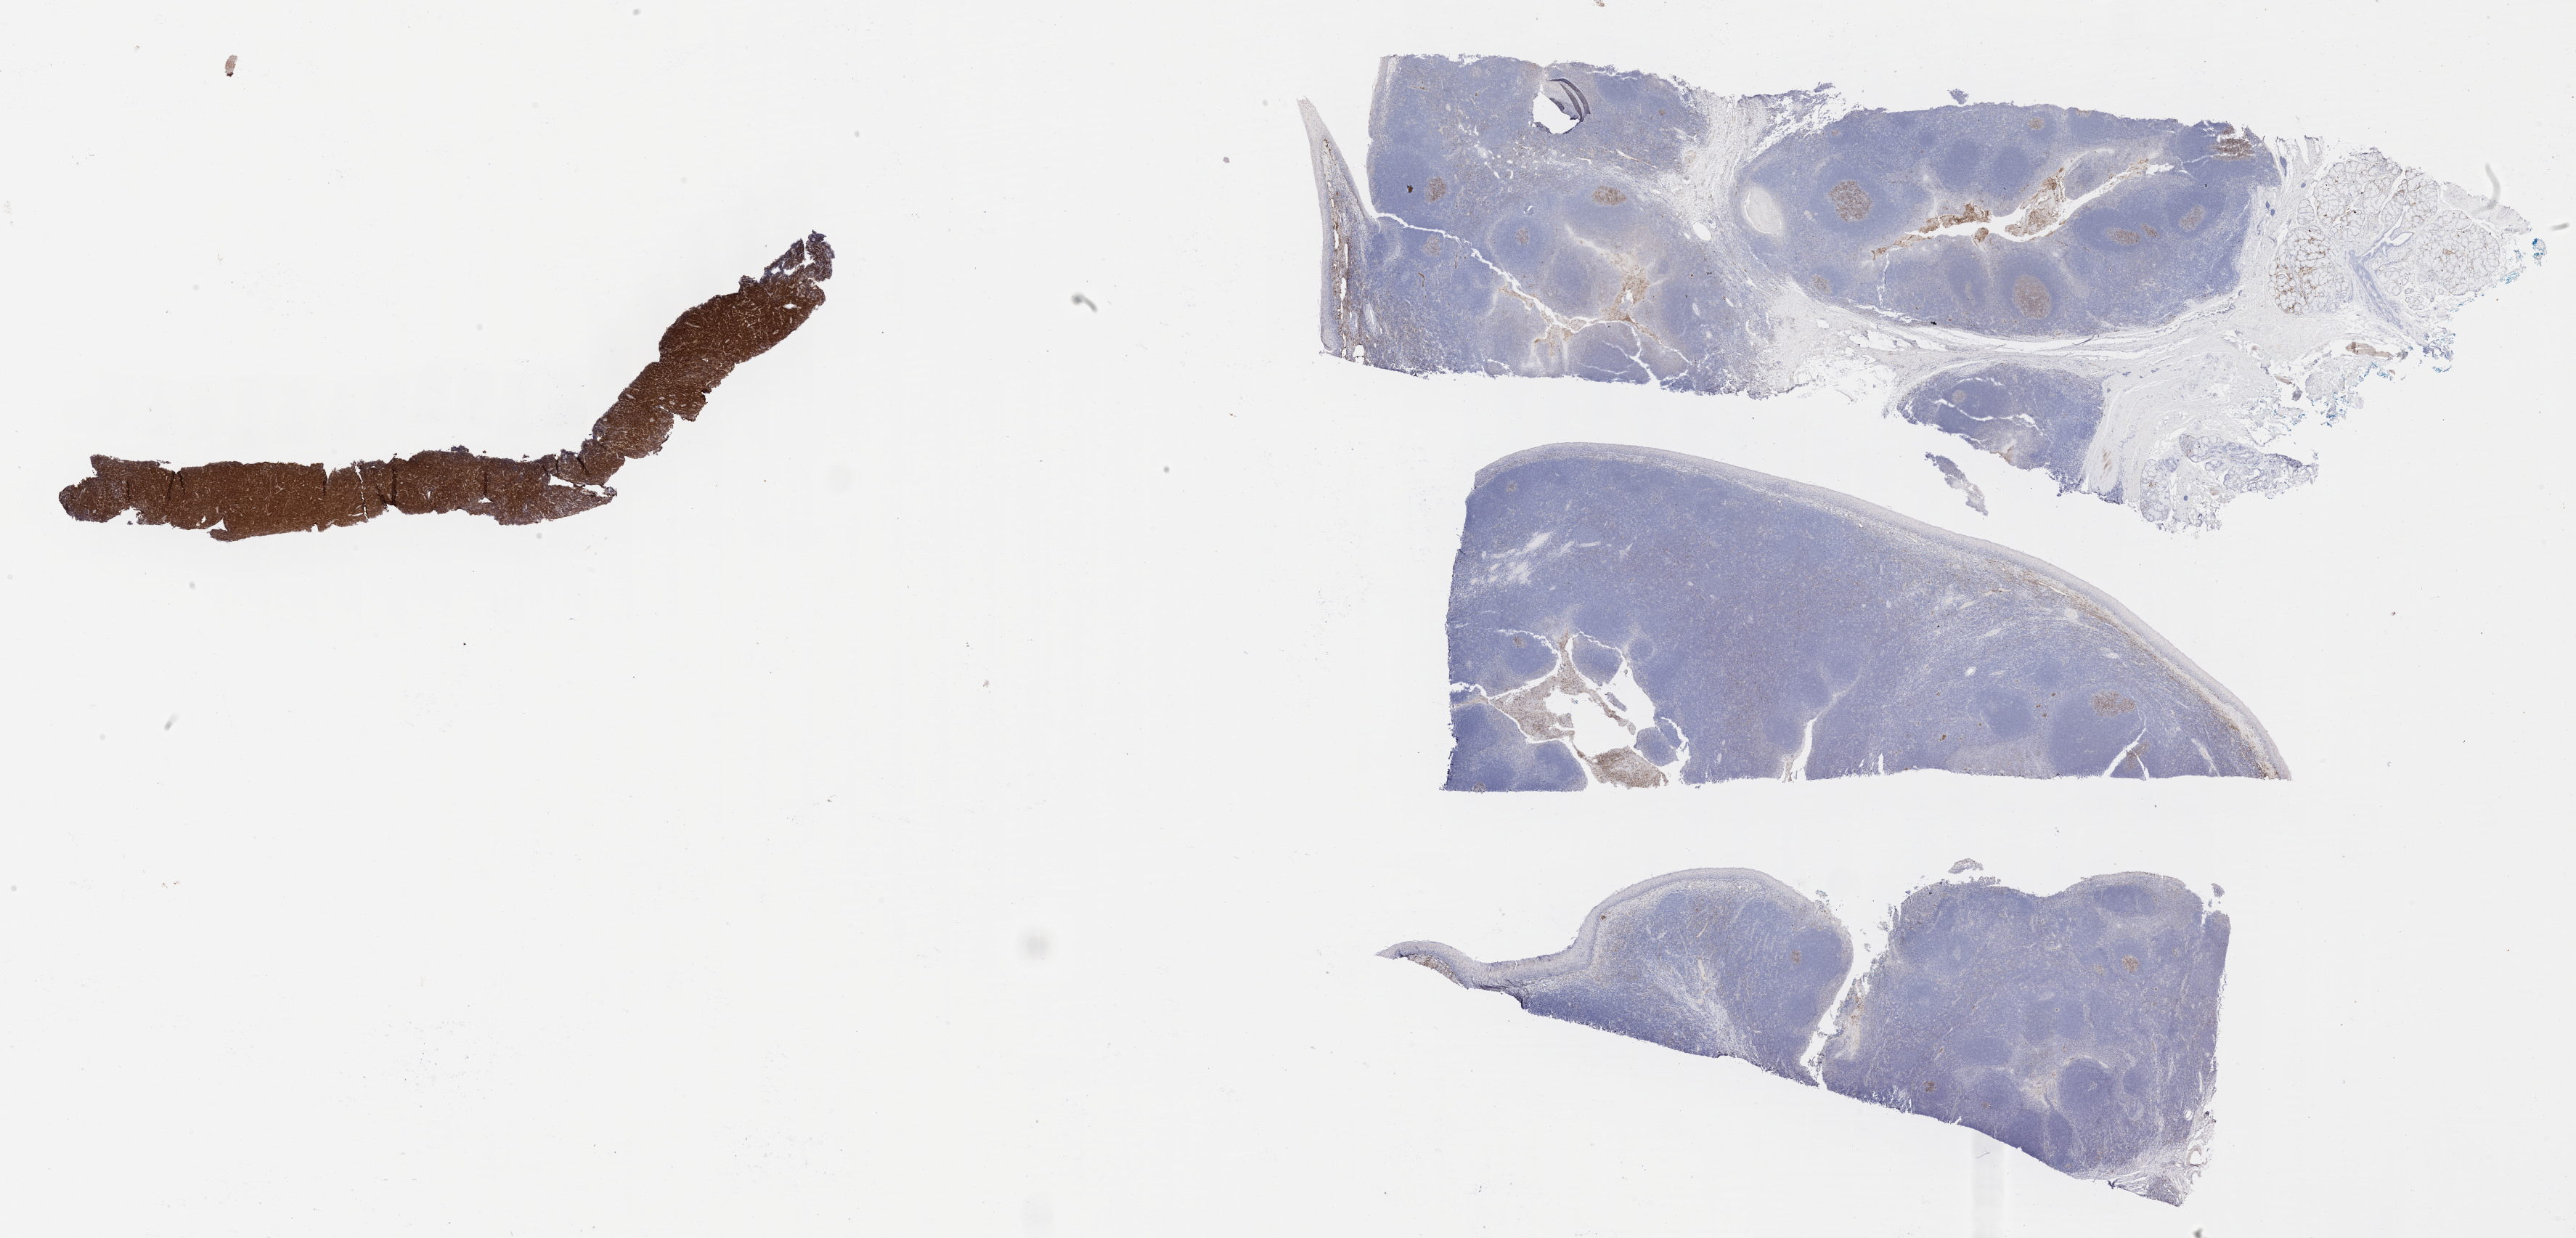
Whole-slide image, immunohistochemical stain for CD10, shown as a low-resolution overview of the whole scanned area (about 28.7 x 13.8 mm). Tumor tissue. Site: kidney. Patient: male, age at initial diagnosis 9 years.
Diagnosis: Burkitt lymphoma, NOS.